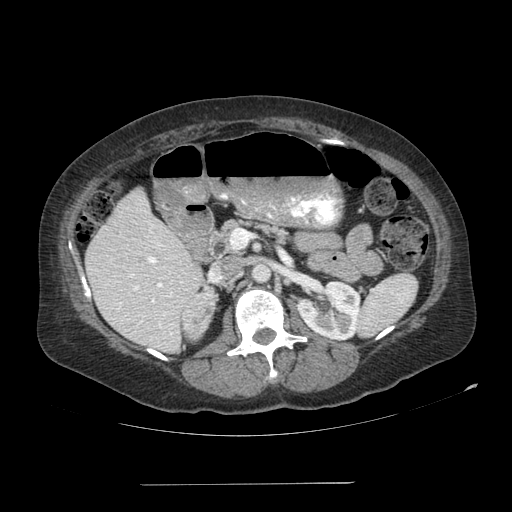
Contrast-enhanced abdominal CT, one axial slice; position 53 of 113 along the scan axis; 120 kVp; soft-tissue window (W 400 / L 40 HU); 2.5 mm slice thickness; 512 × 512 image matrix, field of view 440 × 440 mm. Patient: female, 67 years. Case-level facts recorded for this patient, not image findings: diagnosis: adrenocortical carcinoma; tumour side: right adrenal; tumour size at pathology: 9.8 cm.
Structures marked on this image (semi-automatic segmentation, software-assisted and operator-edited):
- mass: bounding box [x1, y1, x2, y2] px = [183, 294, 213, 341]